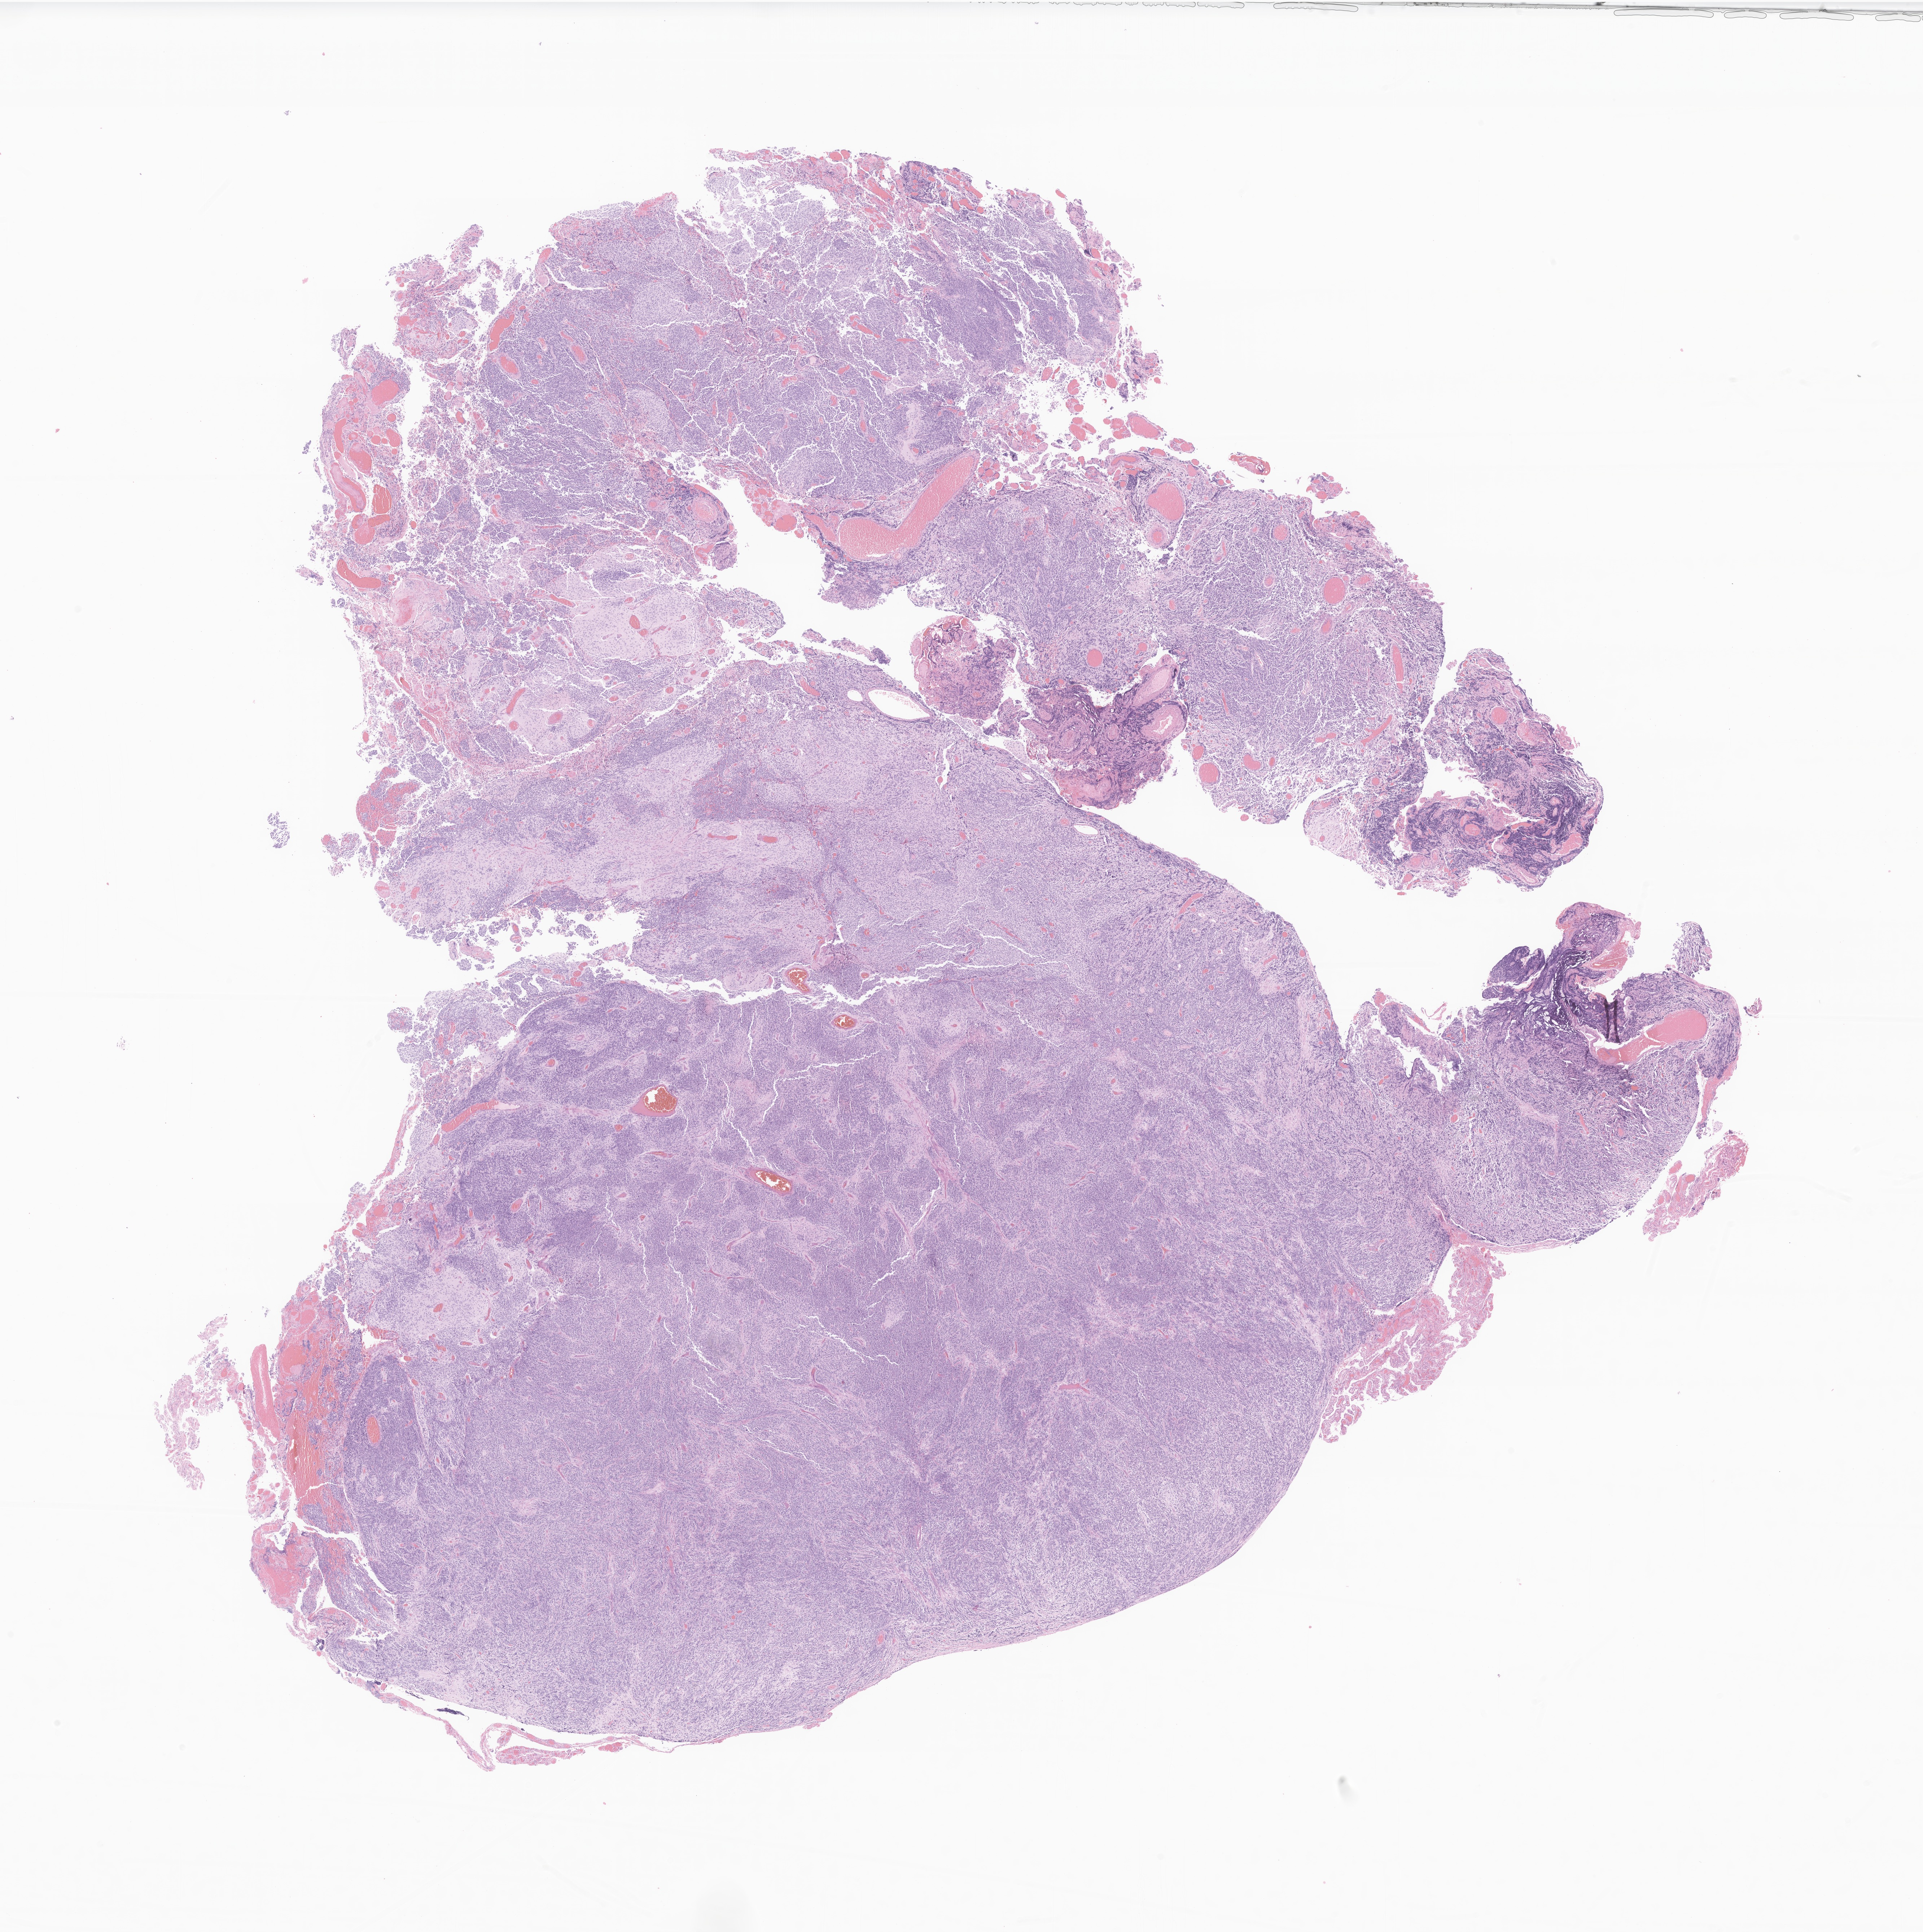
Digitized hematoxylin and eosin (H&E)-stained section of tumor tissue from the brain stem, whole scanned area (about 22.5 x 22.6 mm) shown as a low-resolution overview; formalin-fixed paraffin-embedded section. Patient female; age 251 months (20 years 11 months).
Diagnosis (ICD-O-3 morphology term): Medulloblastoma, NOS.